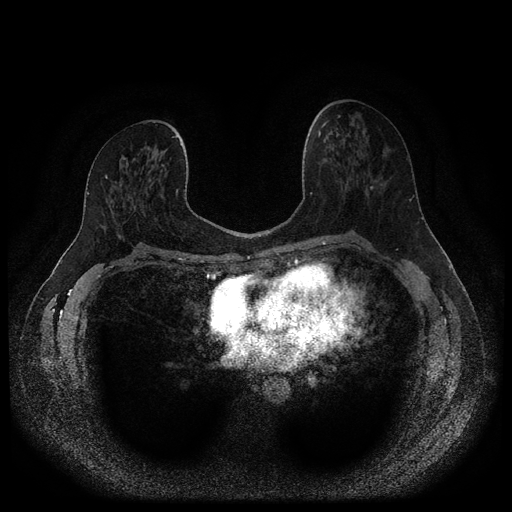
Breast MRI (dynamic contrast-enhanced, multi-phase), one axial slice; dynamic contrast-enhanced series, time point 2 of 5 at this slice position (early post-contrast); 1.5 T; TE 2.7 ms, TR 5.4 ms; 2 mm slice thickness; 512 × 512 image matrix, field of view 330 × 330 mm. Patient: female, 46 years.
Structures marked on this image (semi-automatic segmentation, software-assisted and operator-edited):
- breast lesion (labelled benign in the annotation): bounding box (x1, y1, x2, y2) in pixels: (120, 158, 126, 166)